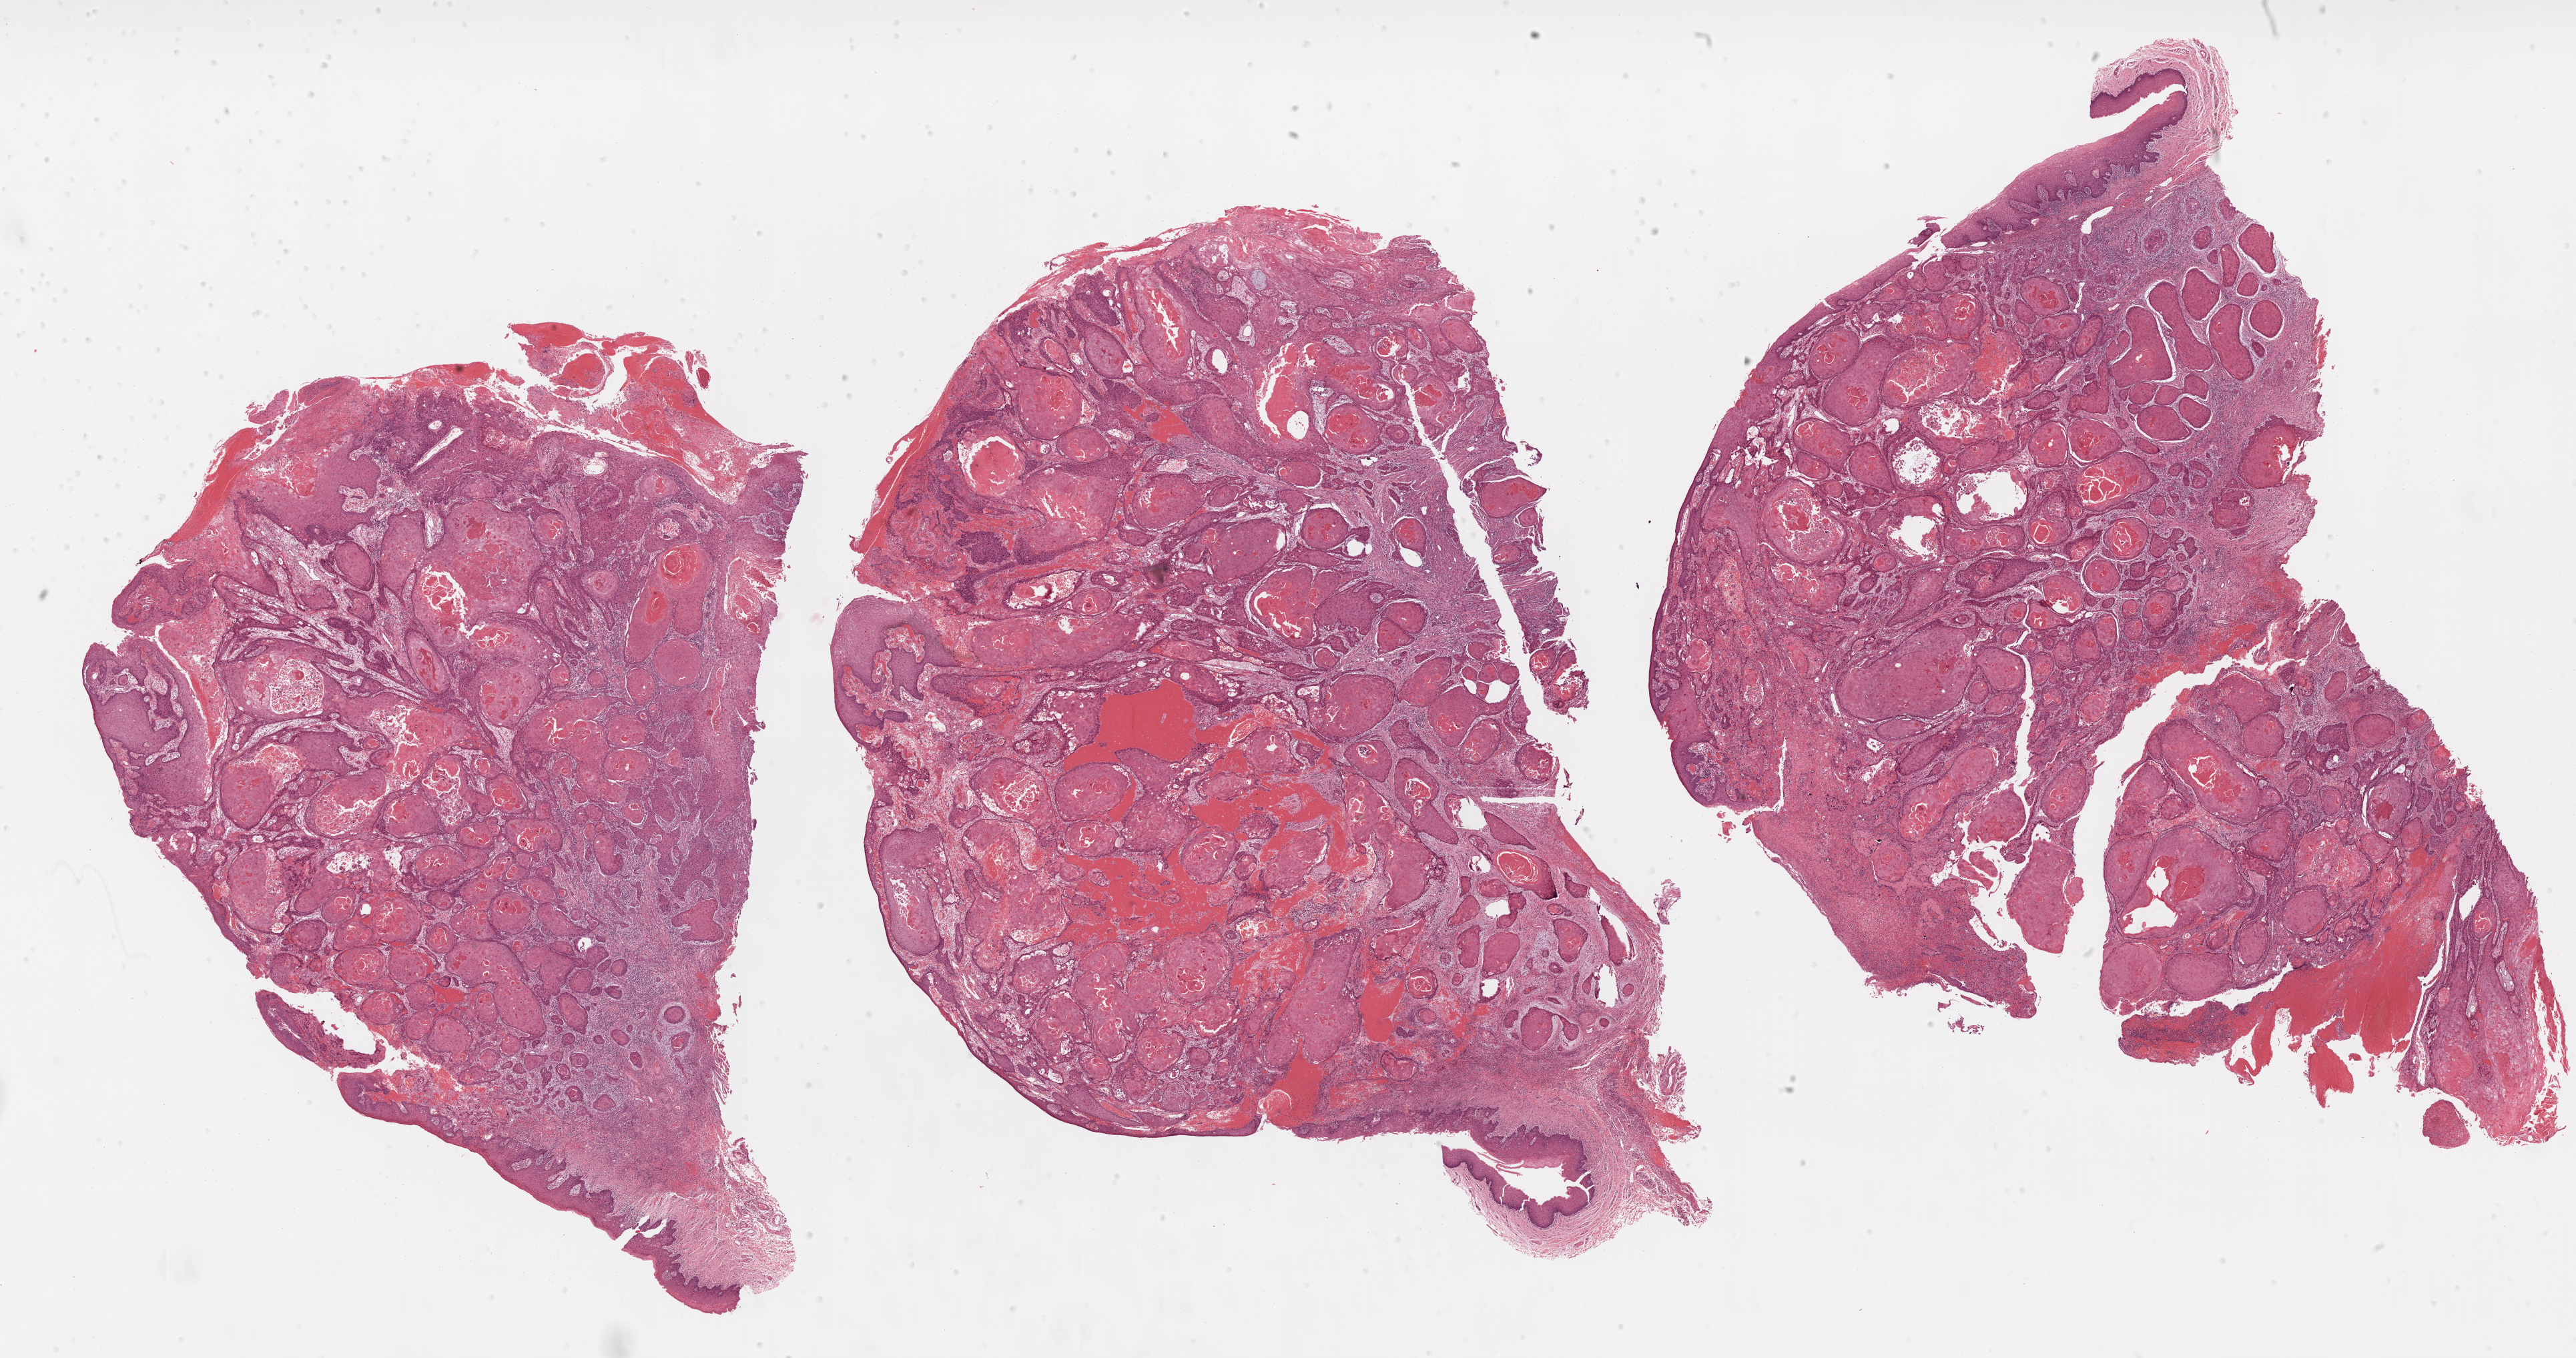
Whole-slide histology image, H&E-stained, shown as a low-resolution overview of the whole scanned area (about 31.0 x 16.3 mm); formalin-fixed paraffin-embedded (FFPE) diagnostic section; sample: primary tumour, head and neck. Female, age 77 years at initial diagnosis. Histologic grade: G2 (moderately differentiated).
- diagnosis: Squamous cell carcinoma, NOS
- AJCC pathologic stage: II